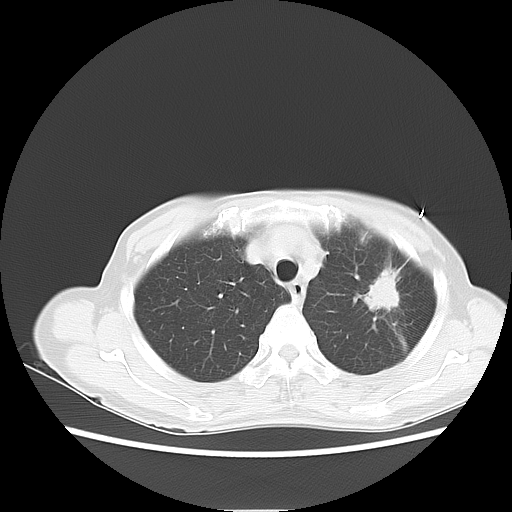
Chest CT, one axial slice; position 9 of 14 along the scan axis; reconstruction kernel LUNG; 120 kVp; lung window (W 1500 / L -600 HU); 512 × 512 image matrix, field of view 350 × 350 mm. Female patient, age 71 years. Case-level facts recorded for this patient, not image findings: clinical TNM (as recorded): T2 N0 M0.
Annotated regions visible in this slice (rectangle marked by the reading radiologist):
- lung tumour (recorded histology: adenocarcinoma): bounding box (x1, y1, x2, y2) in pixels: (360, 263, 410, 321)